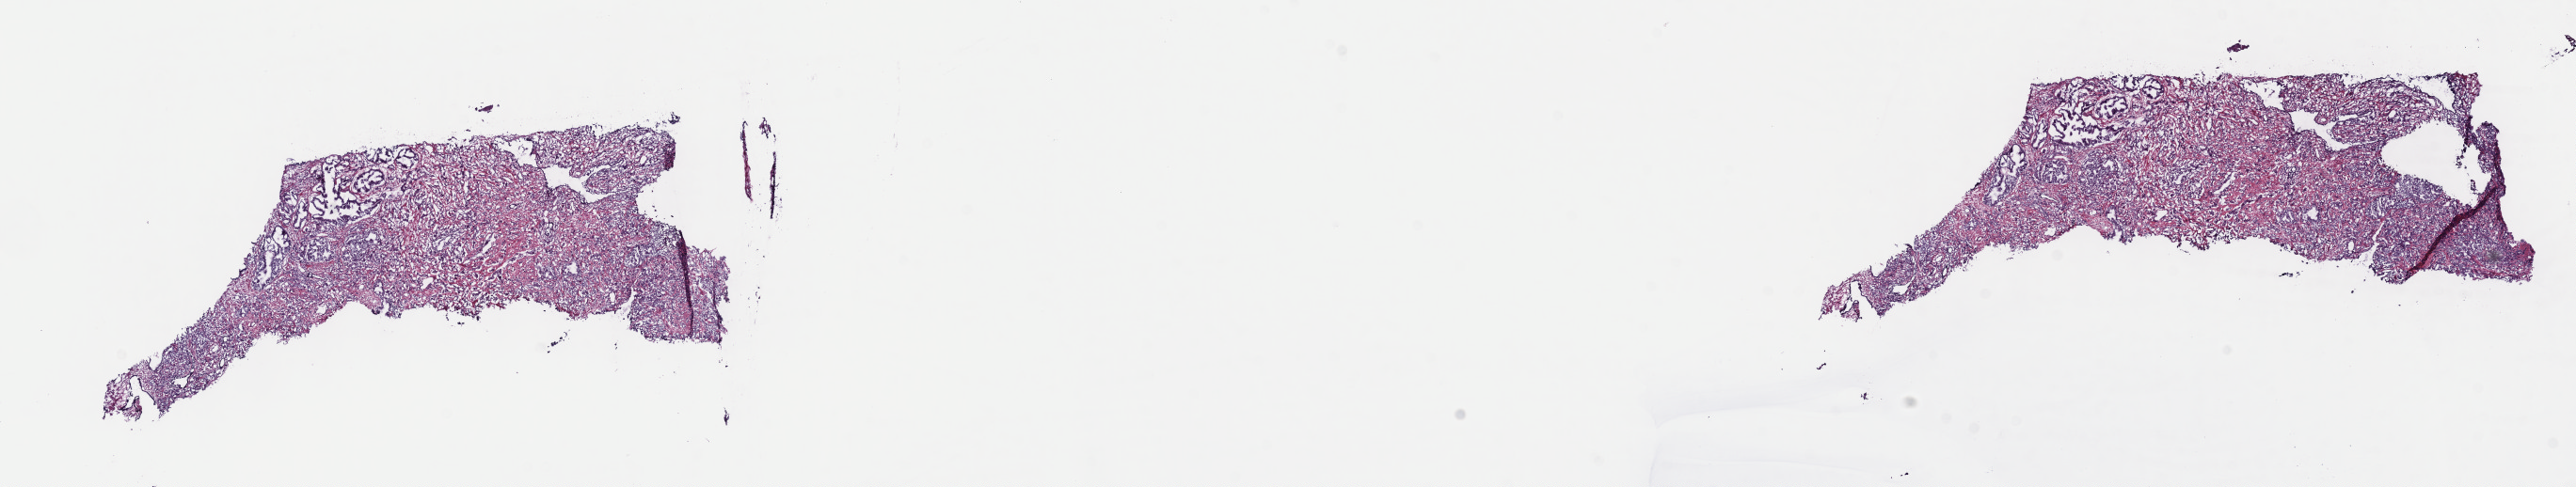
H&E-stained whole-slide image — whole scanned area (about 22.1 x 4.2 mm, from a 40x scan) shown as a low-resolution overview. Frozen section from the top of the tissue portion. Prostate, primary tumour sample. Patient: male, age at initial diagnosis 63 years. Gleason score: 9 (4+5). Slide review estimates, as recorded: tumour cells 80%, tumour nuclei 80%, normal cells 0%, stromal cells 20%, necrosis 0%. Inflammatory infiltration, as recorded: lymphocyte infiltration 0%, monocyte infiltration 0%, neutrophil infiltration 0%.
Pathologic diagnosis: Adenocarcinoma, NOS (prostate gland). Laterality: bilateral. Lymph nodes positive (case pathology): 0 of 29 examined.